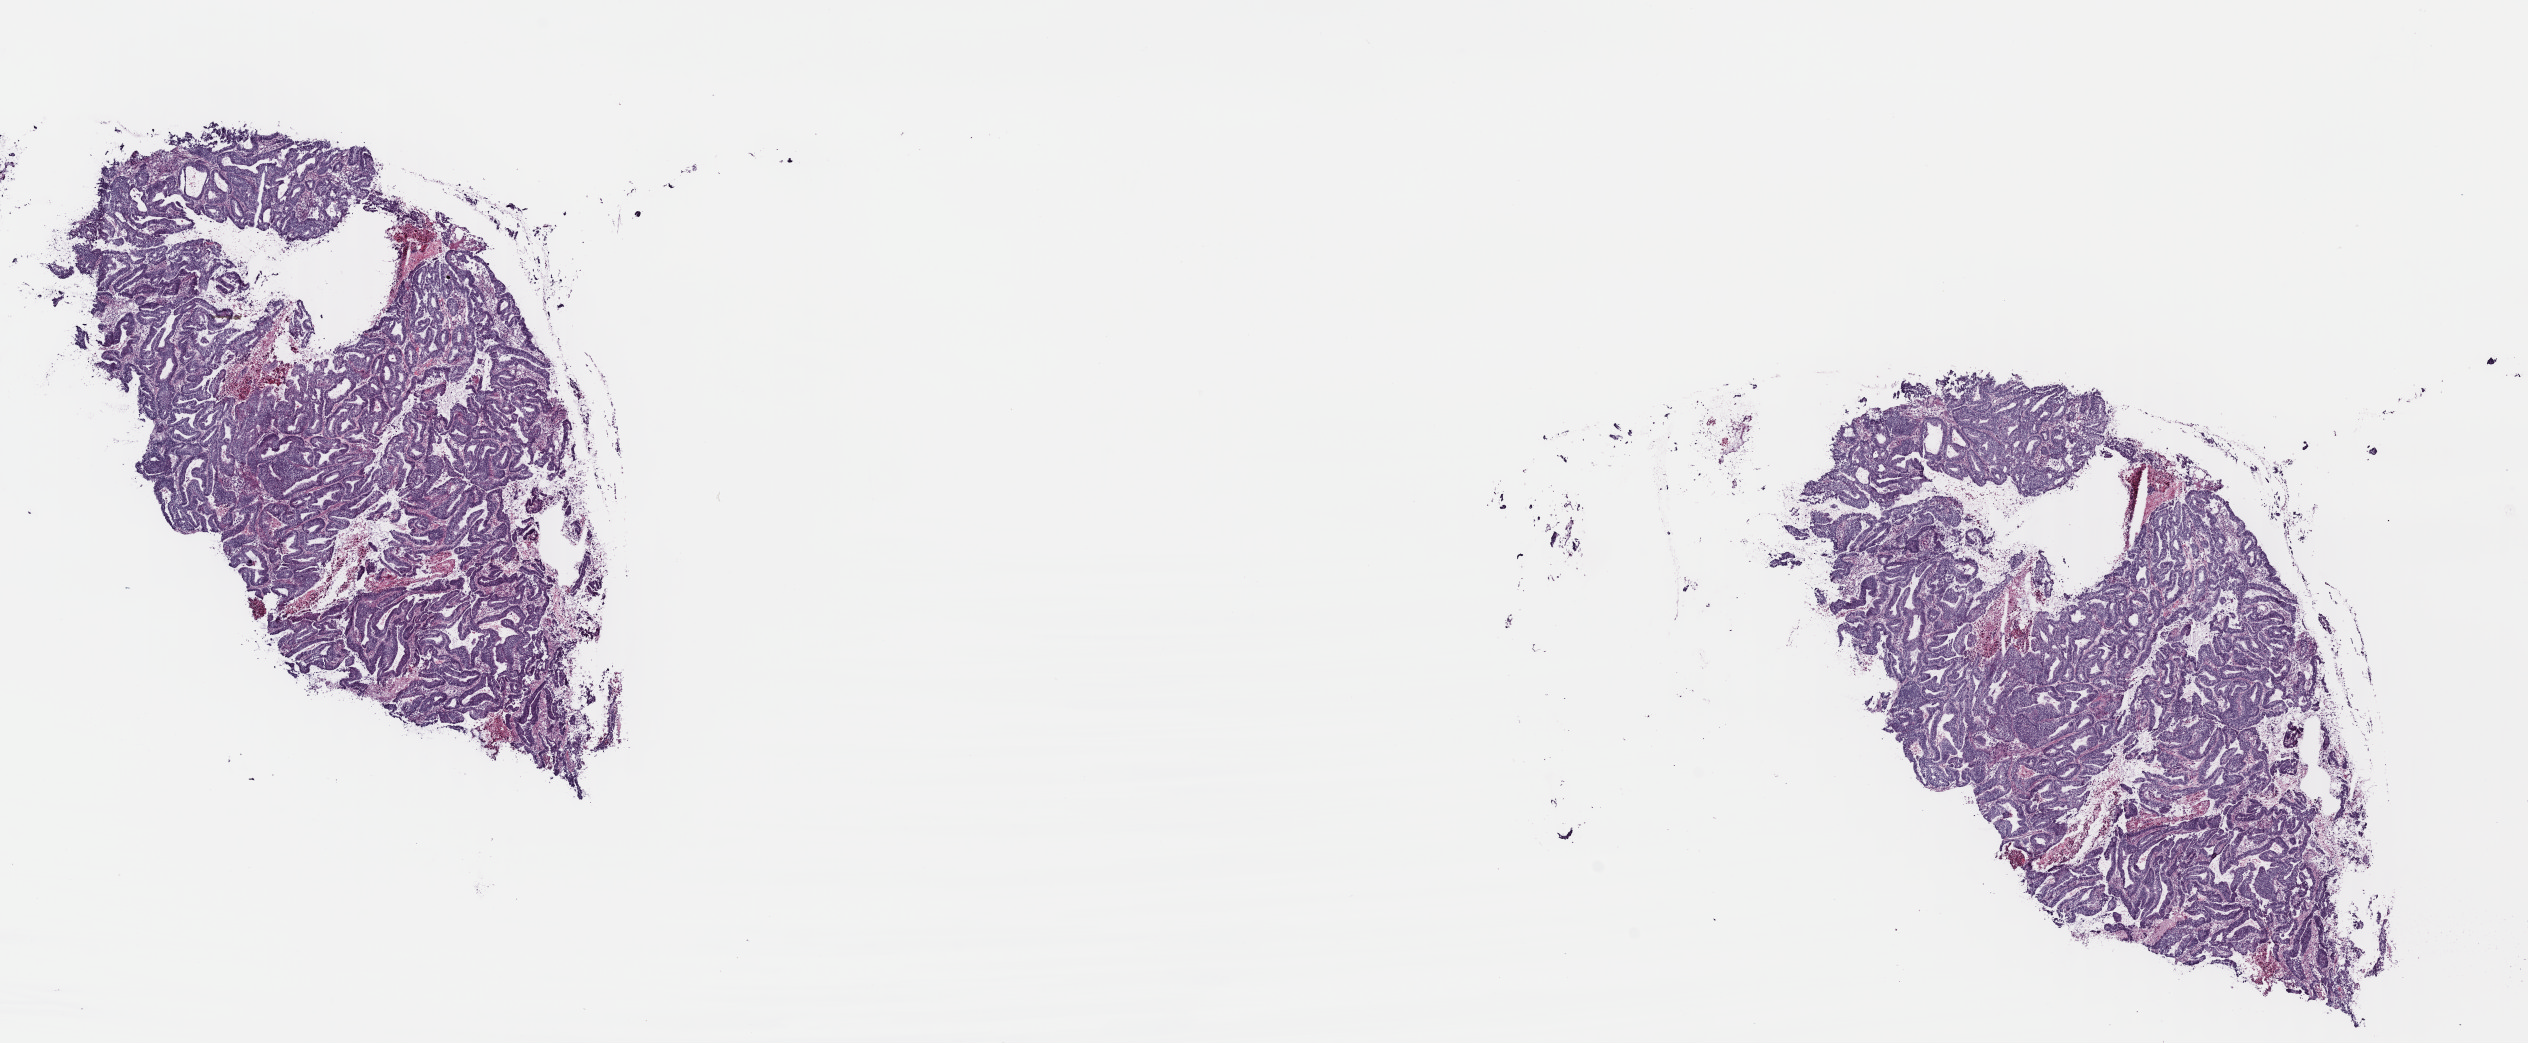
H&E whole-slide image, a low-resolution overview of the entire scanned area, about 19.9 x 8.2 mm; frozen section from the top of the tissue portion; primary tumour sample from the uterus. Female, age 72 years at initial diagnosis. Histologic grade: G3 (poorly differentiated). Composition of this section per pathologist review: tumour cells 80%, tumour nuclei 80%, normal cells 0%, stromal cells 20%, necrosis 0%. Inflammatory infiltration, as recorded: lymphocyte infiltration 0%, monocyte infiltration 0%, neutrophil infiltration 0%.
- histologic diagnosis: Endometrioid adenocarcinoma, NOS
- lymph nodes positive (case pathology): 0 of 16 examined
- FIGO stage: IB